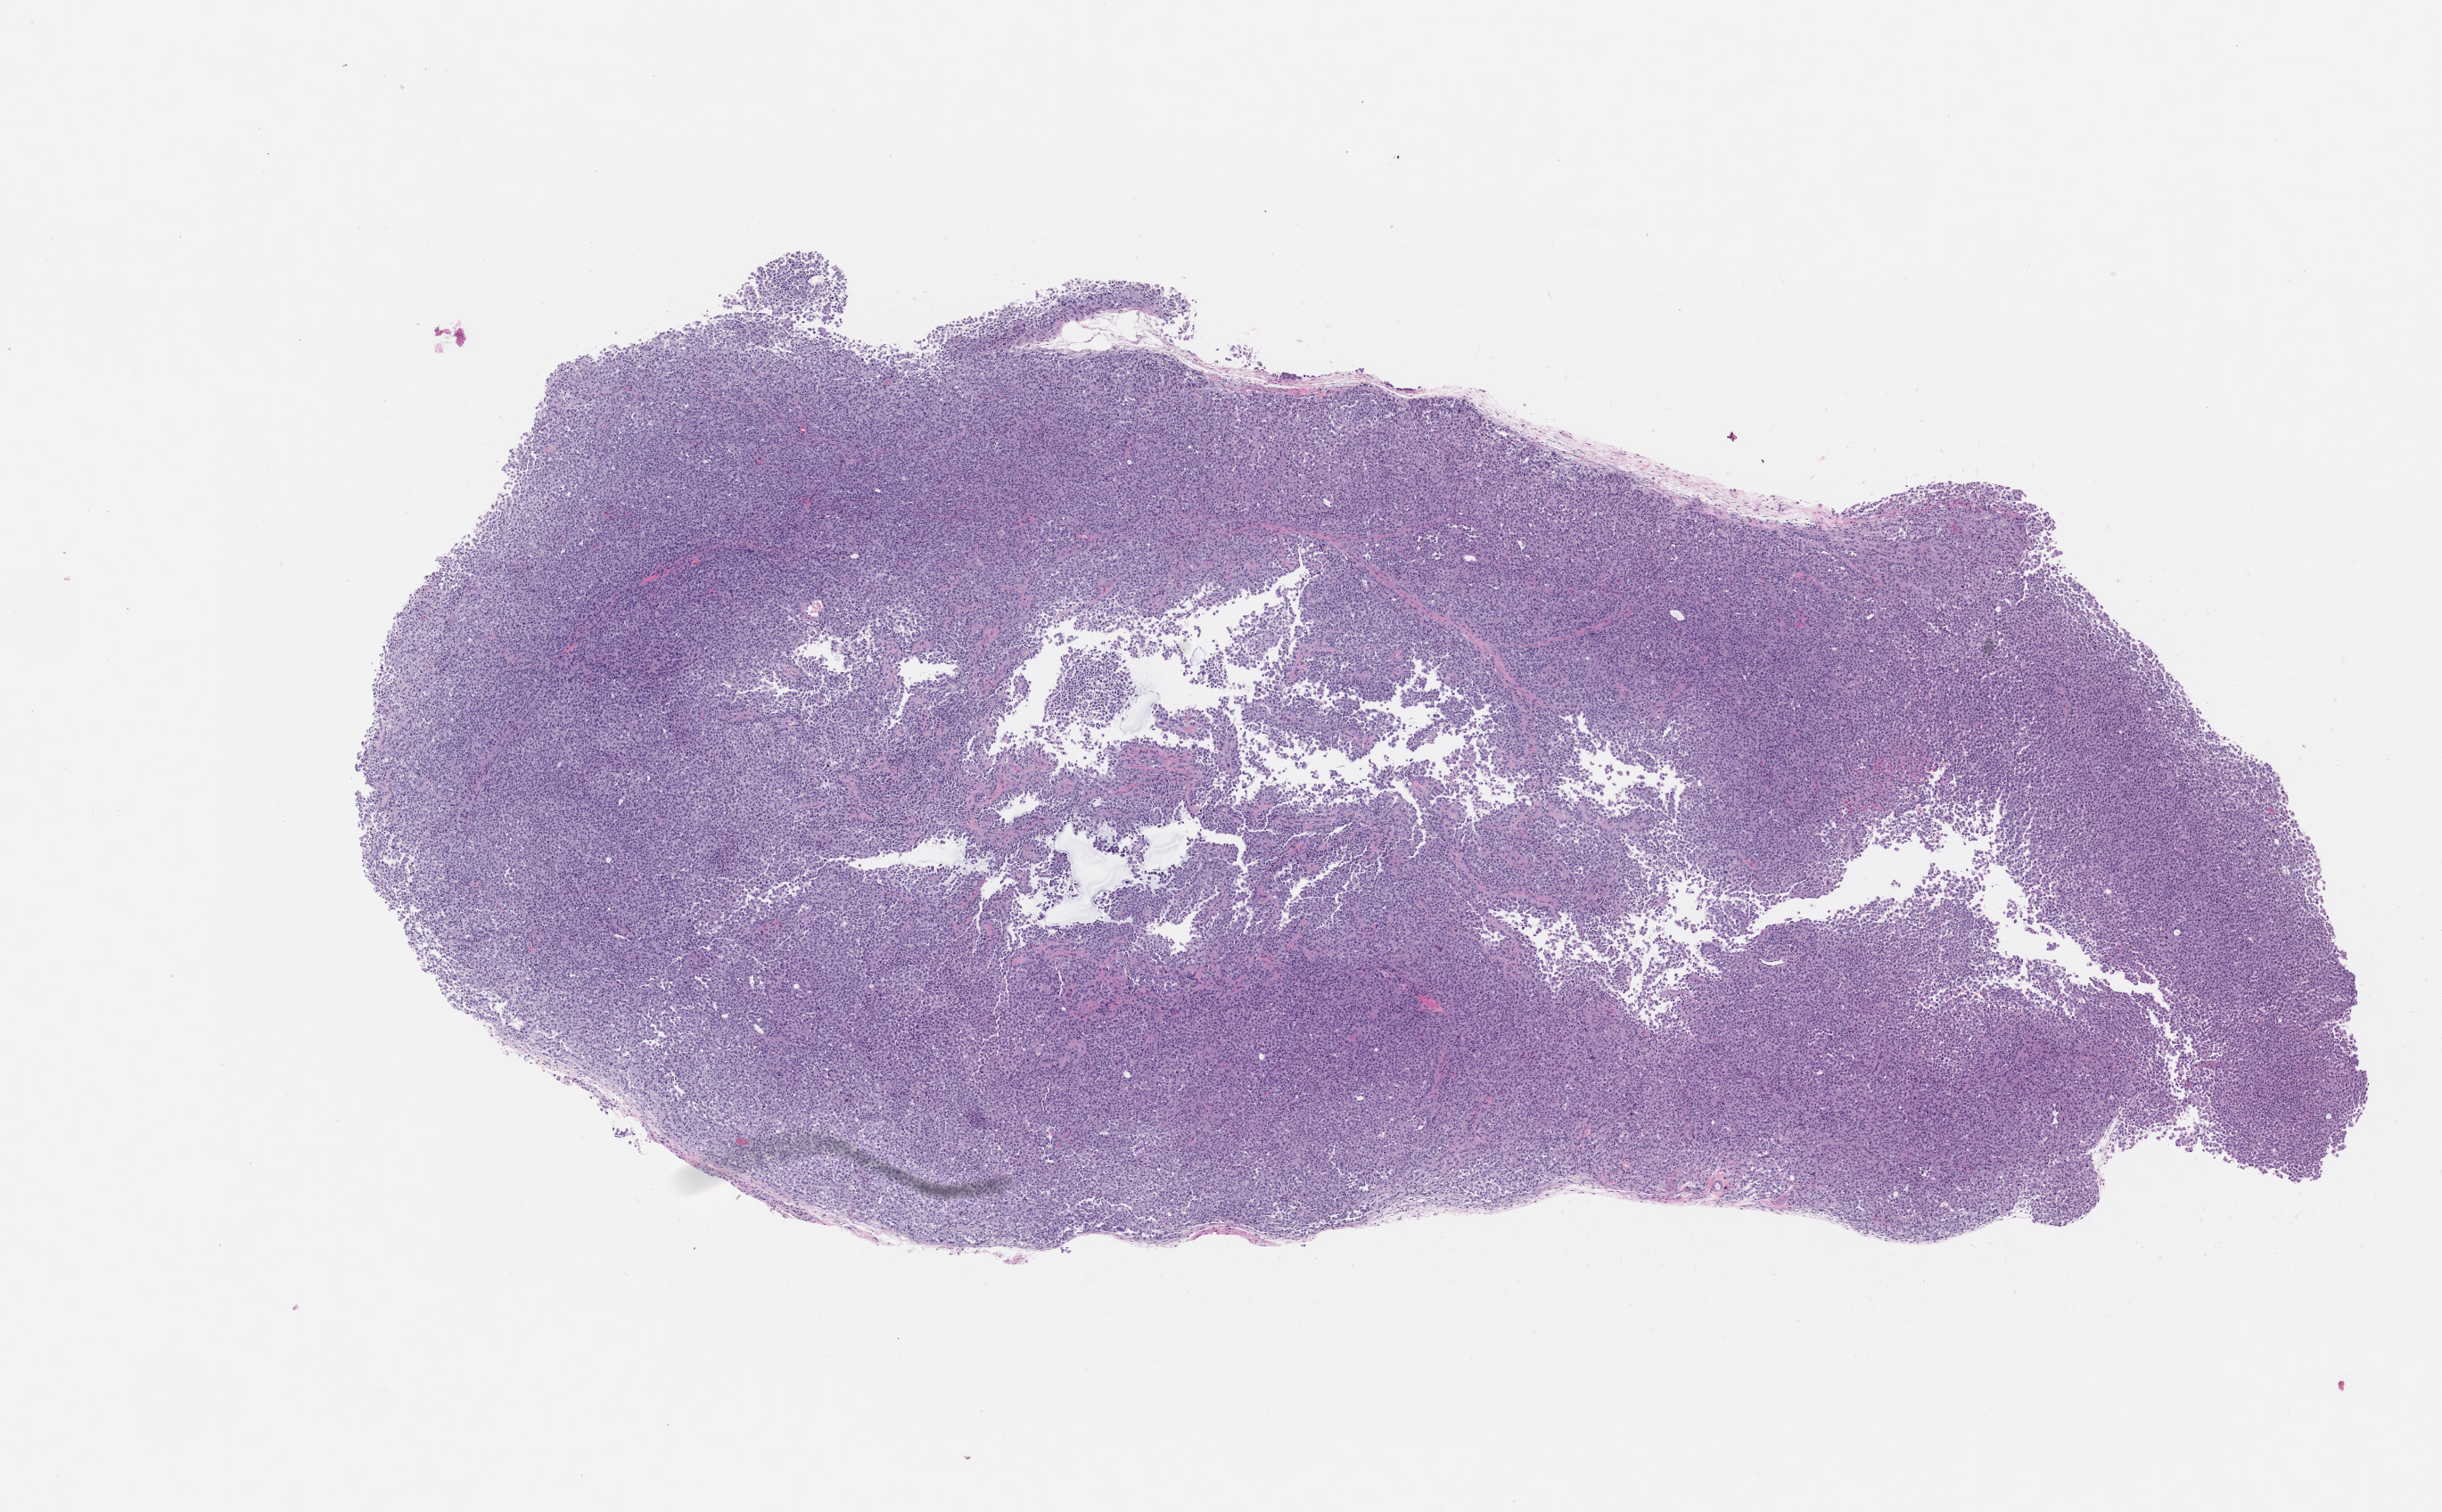
Whole-slide image, H&E: patient-derived xenograft (human tumor grown in a mouse), passage 1, a low-resolution overview of the entire scanned area, about 11.0 x 6.8 mm; FFPE section.
Originating patient diagnosis: Mesothelial Neoplasm.